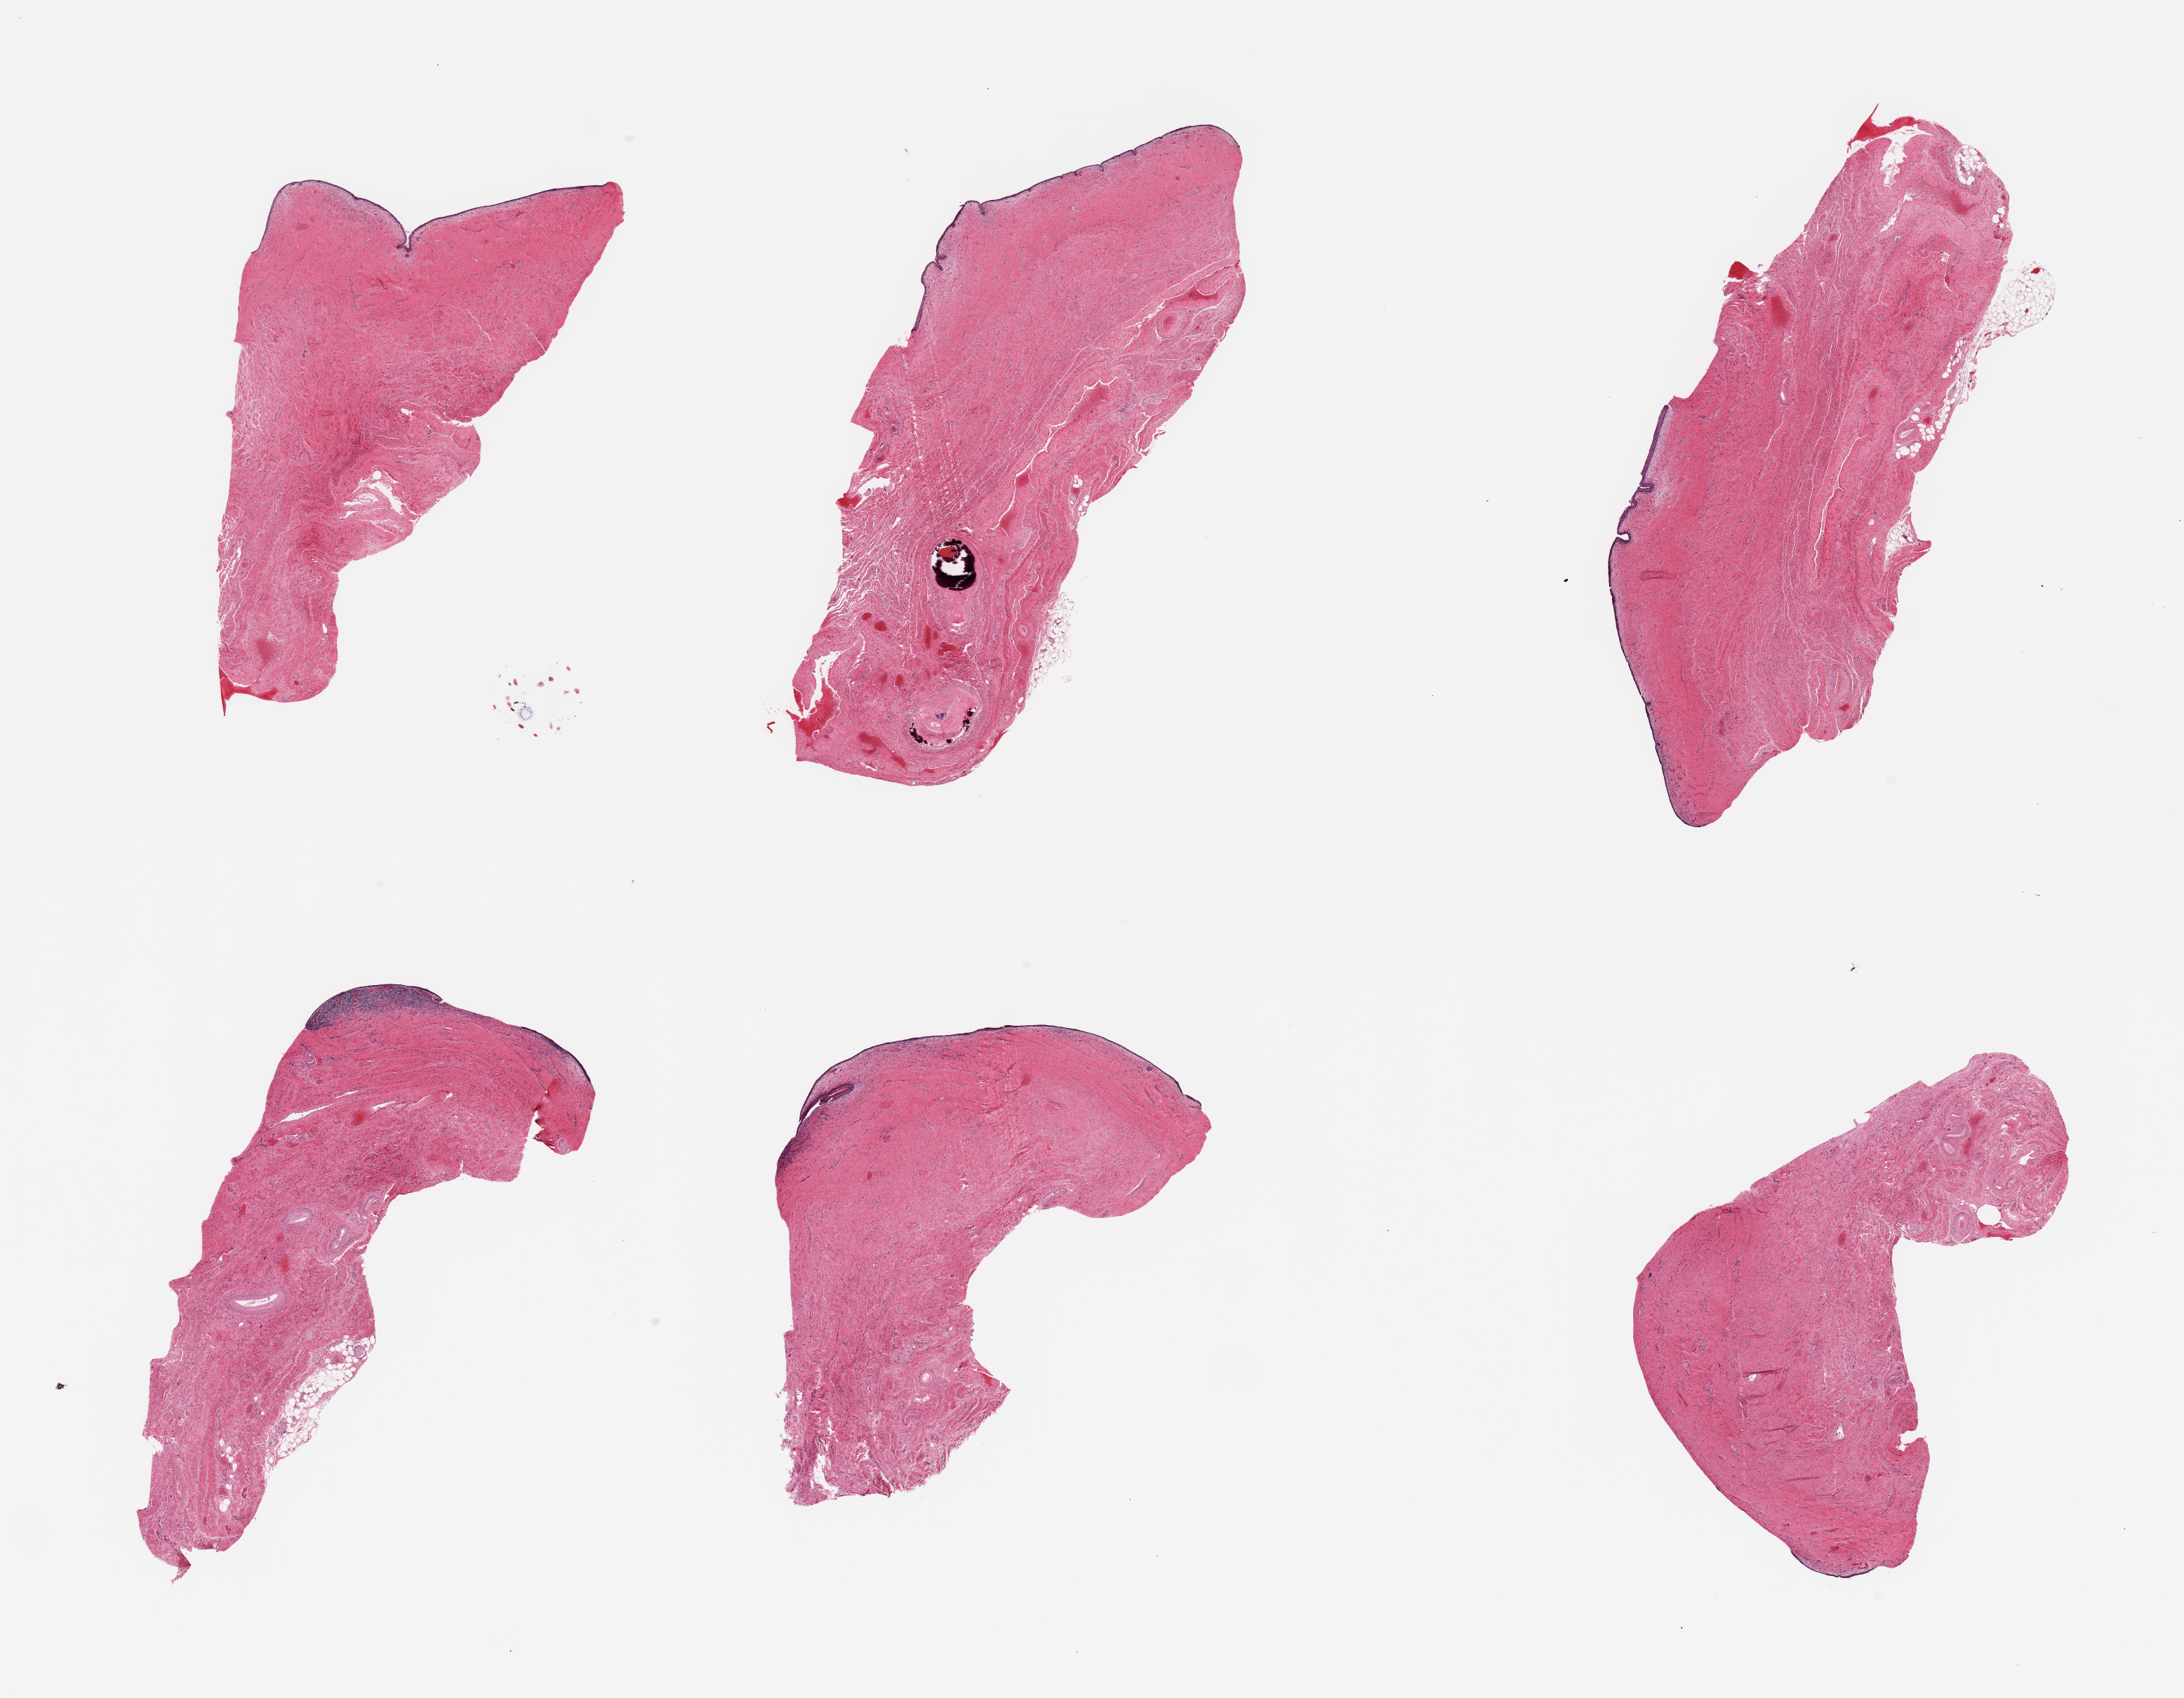
Whole-slide image, H&E stain, brightfield, whole scanned area (about 24.6 x 19.1 mm) shown as a low-resolution overview; PAXgene-fixed, paraffin-embedded tissue; section of vagina (target tissue); tissue donor sample. Female donor.
Pathologist's review note for this sample: 6 pieces squamous mucosa atrophic, partly sloughed; Ectopic stromal calcification, ~0.5mm, unknown etiology, but benign.